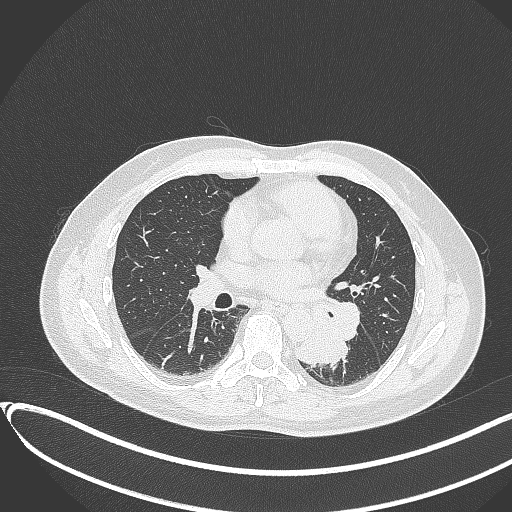
Chest CT, one axial slice; position 174 of 417 along the scan axis; reconstruction kernel B70f; 120 kVp; lung window (W 1500 / L -600 HU); 1 mm slice thickness; 512 × 512 image matrix, field of view 400 × 400 mm. Male patient, age 54 years. Case-level facts recorded for this patient, not image findings: clinical TNM (as recorded): T3 N0 M0.
Annotated regions visible in this slice (bounding box drawn by a radiologist):
- lung tumour (recorded histology: squamous cell carcinoma): bounding box [x1, y1, x2, y2] px = [295, 307, 354, 368]